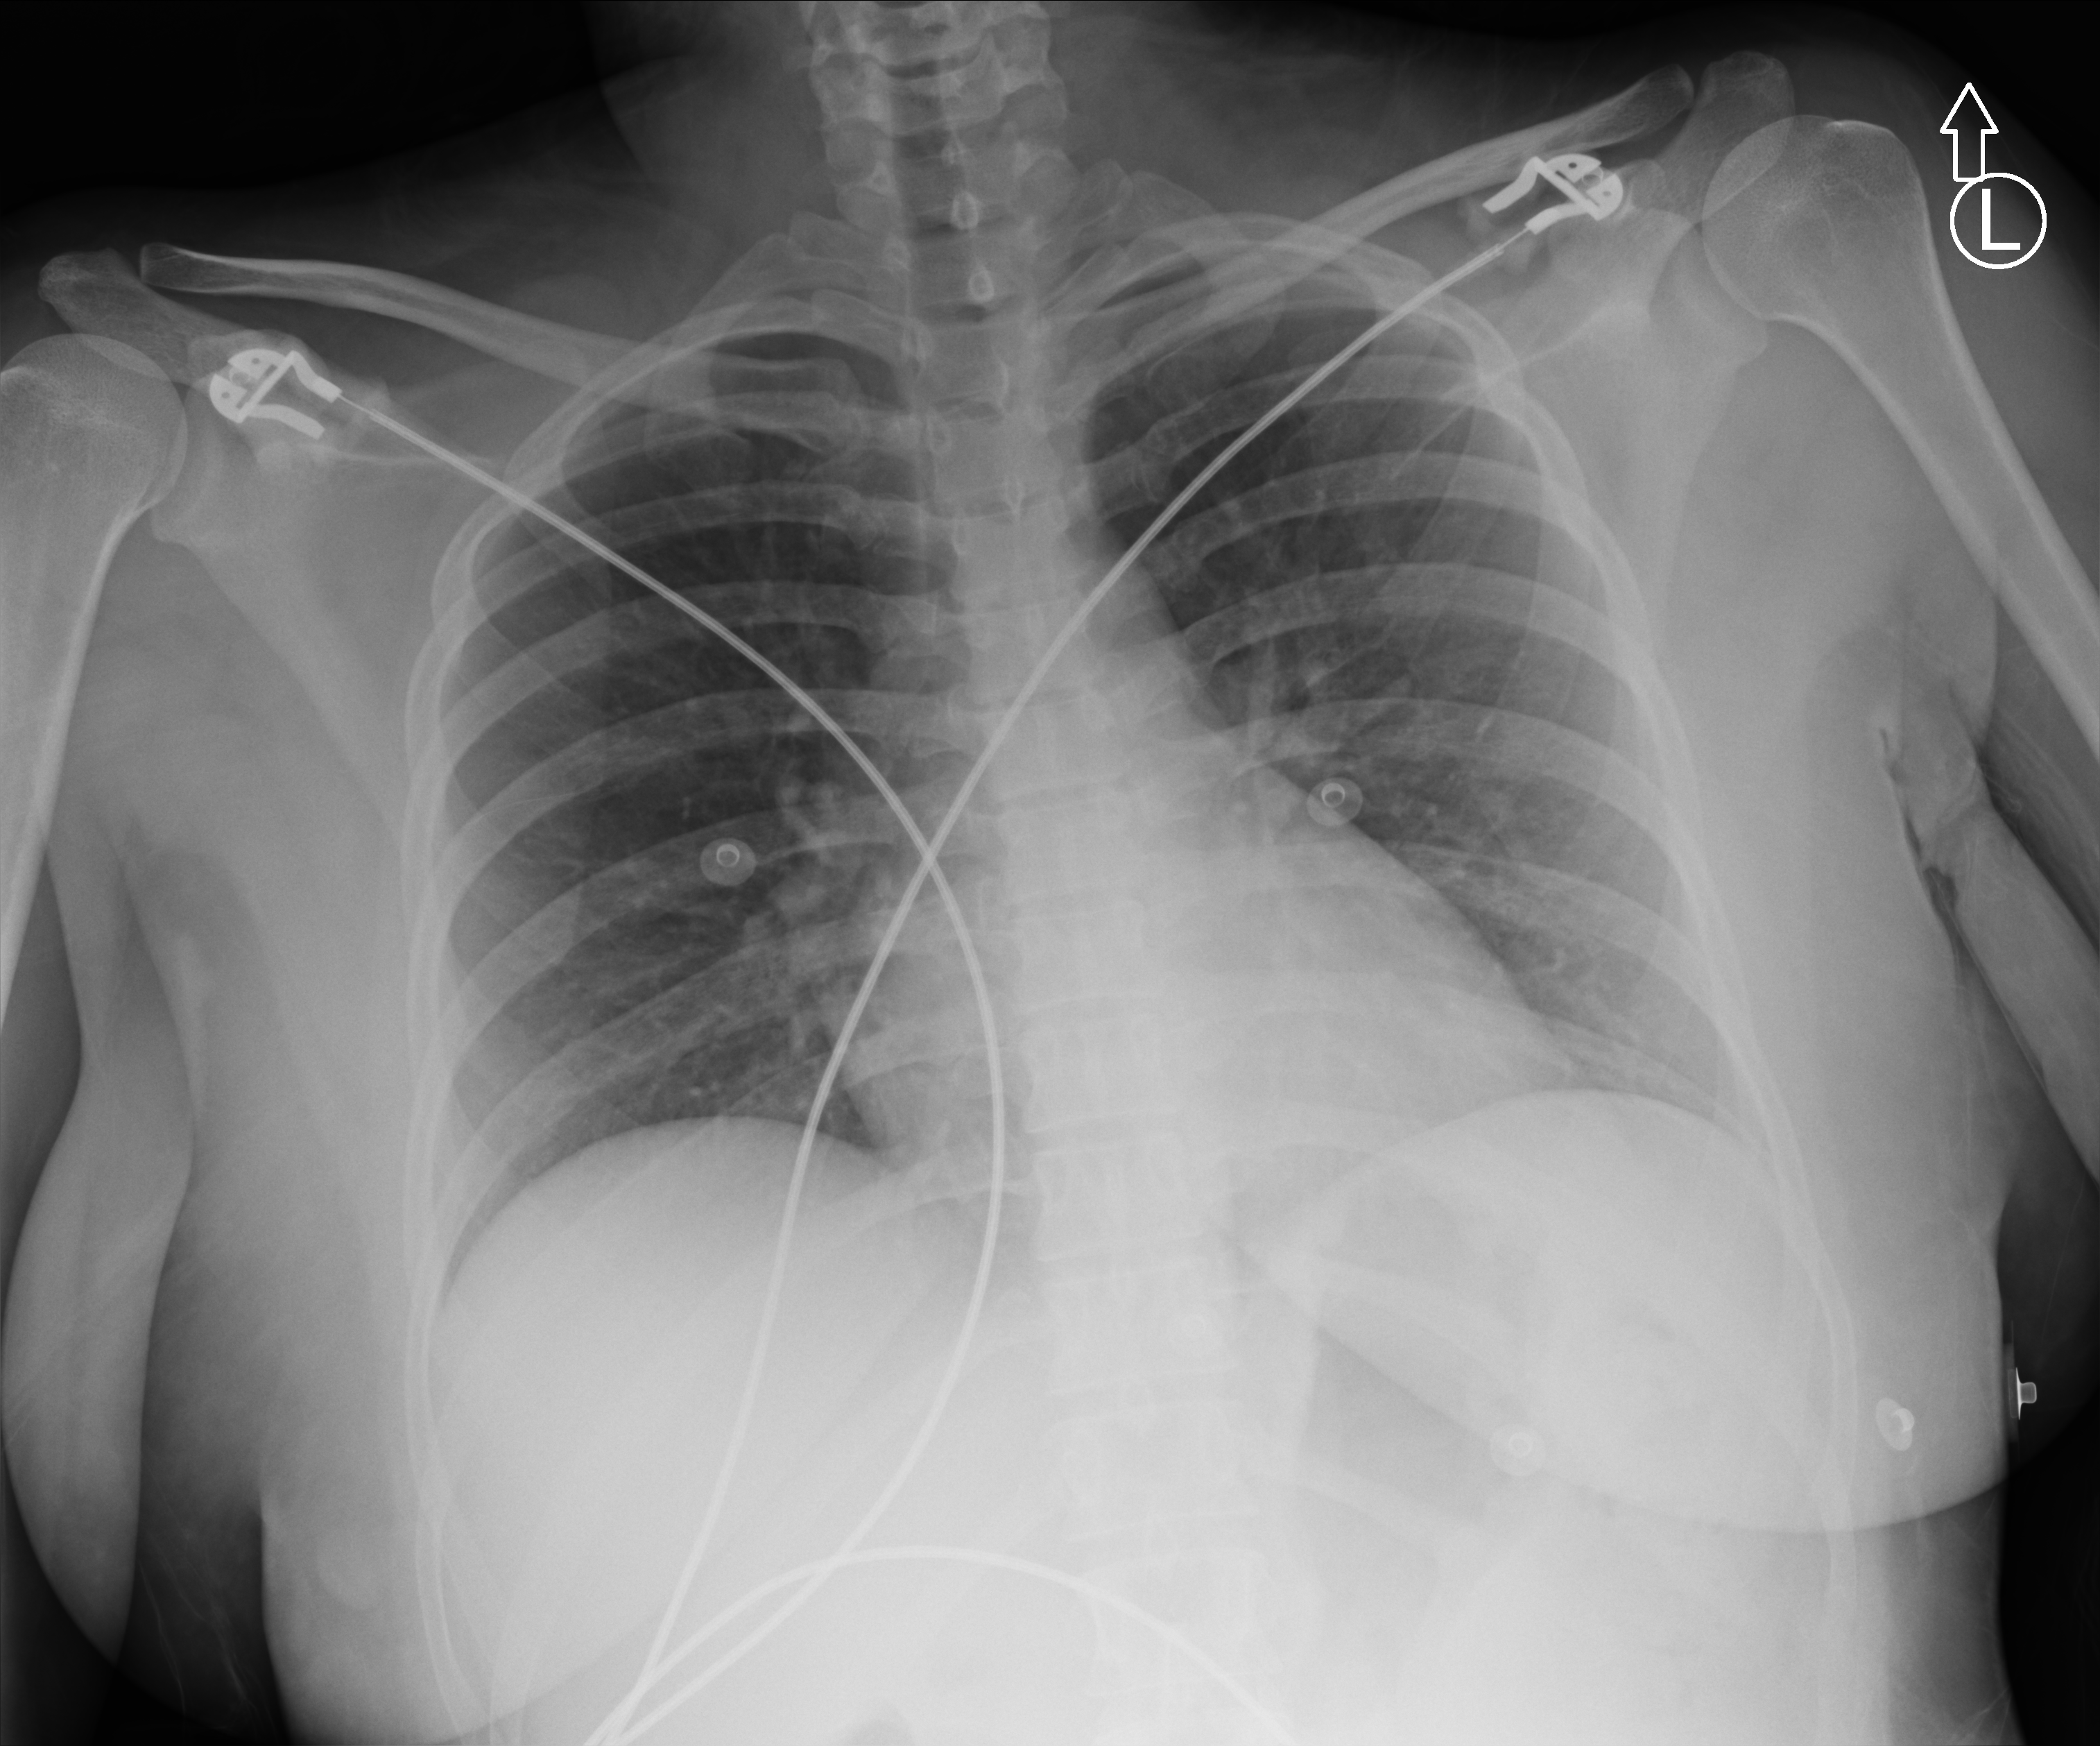
Portable chest radiograph; anteroposterior (AP) projection. Female patient hospitalised with COVID-19, age 18–59 years.
From the hospital-stay record, not from the radiograph (when in the stay this image was taken is not recorded):
- admitted to intensive care during this hospital stay: no